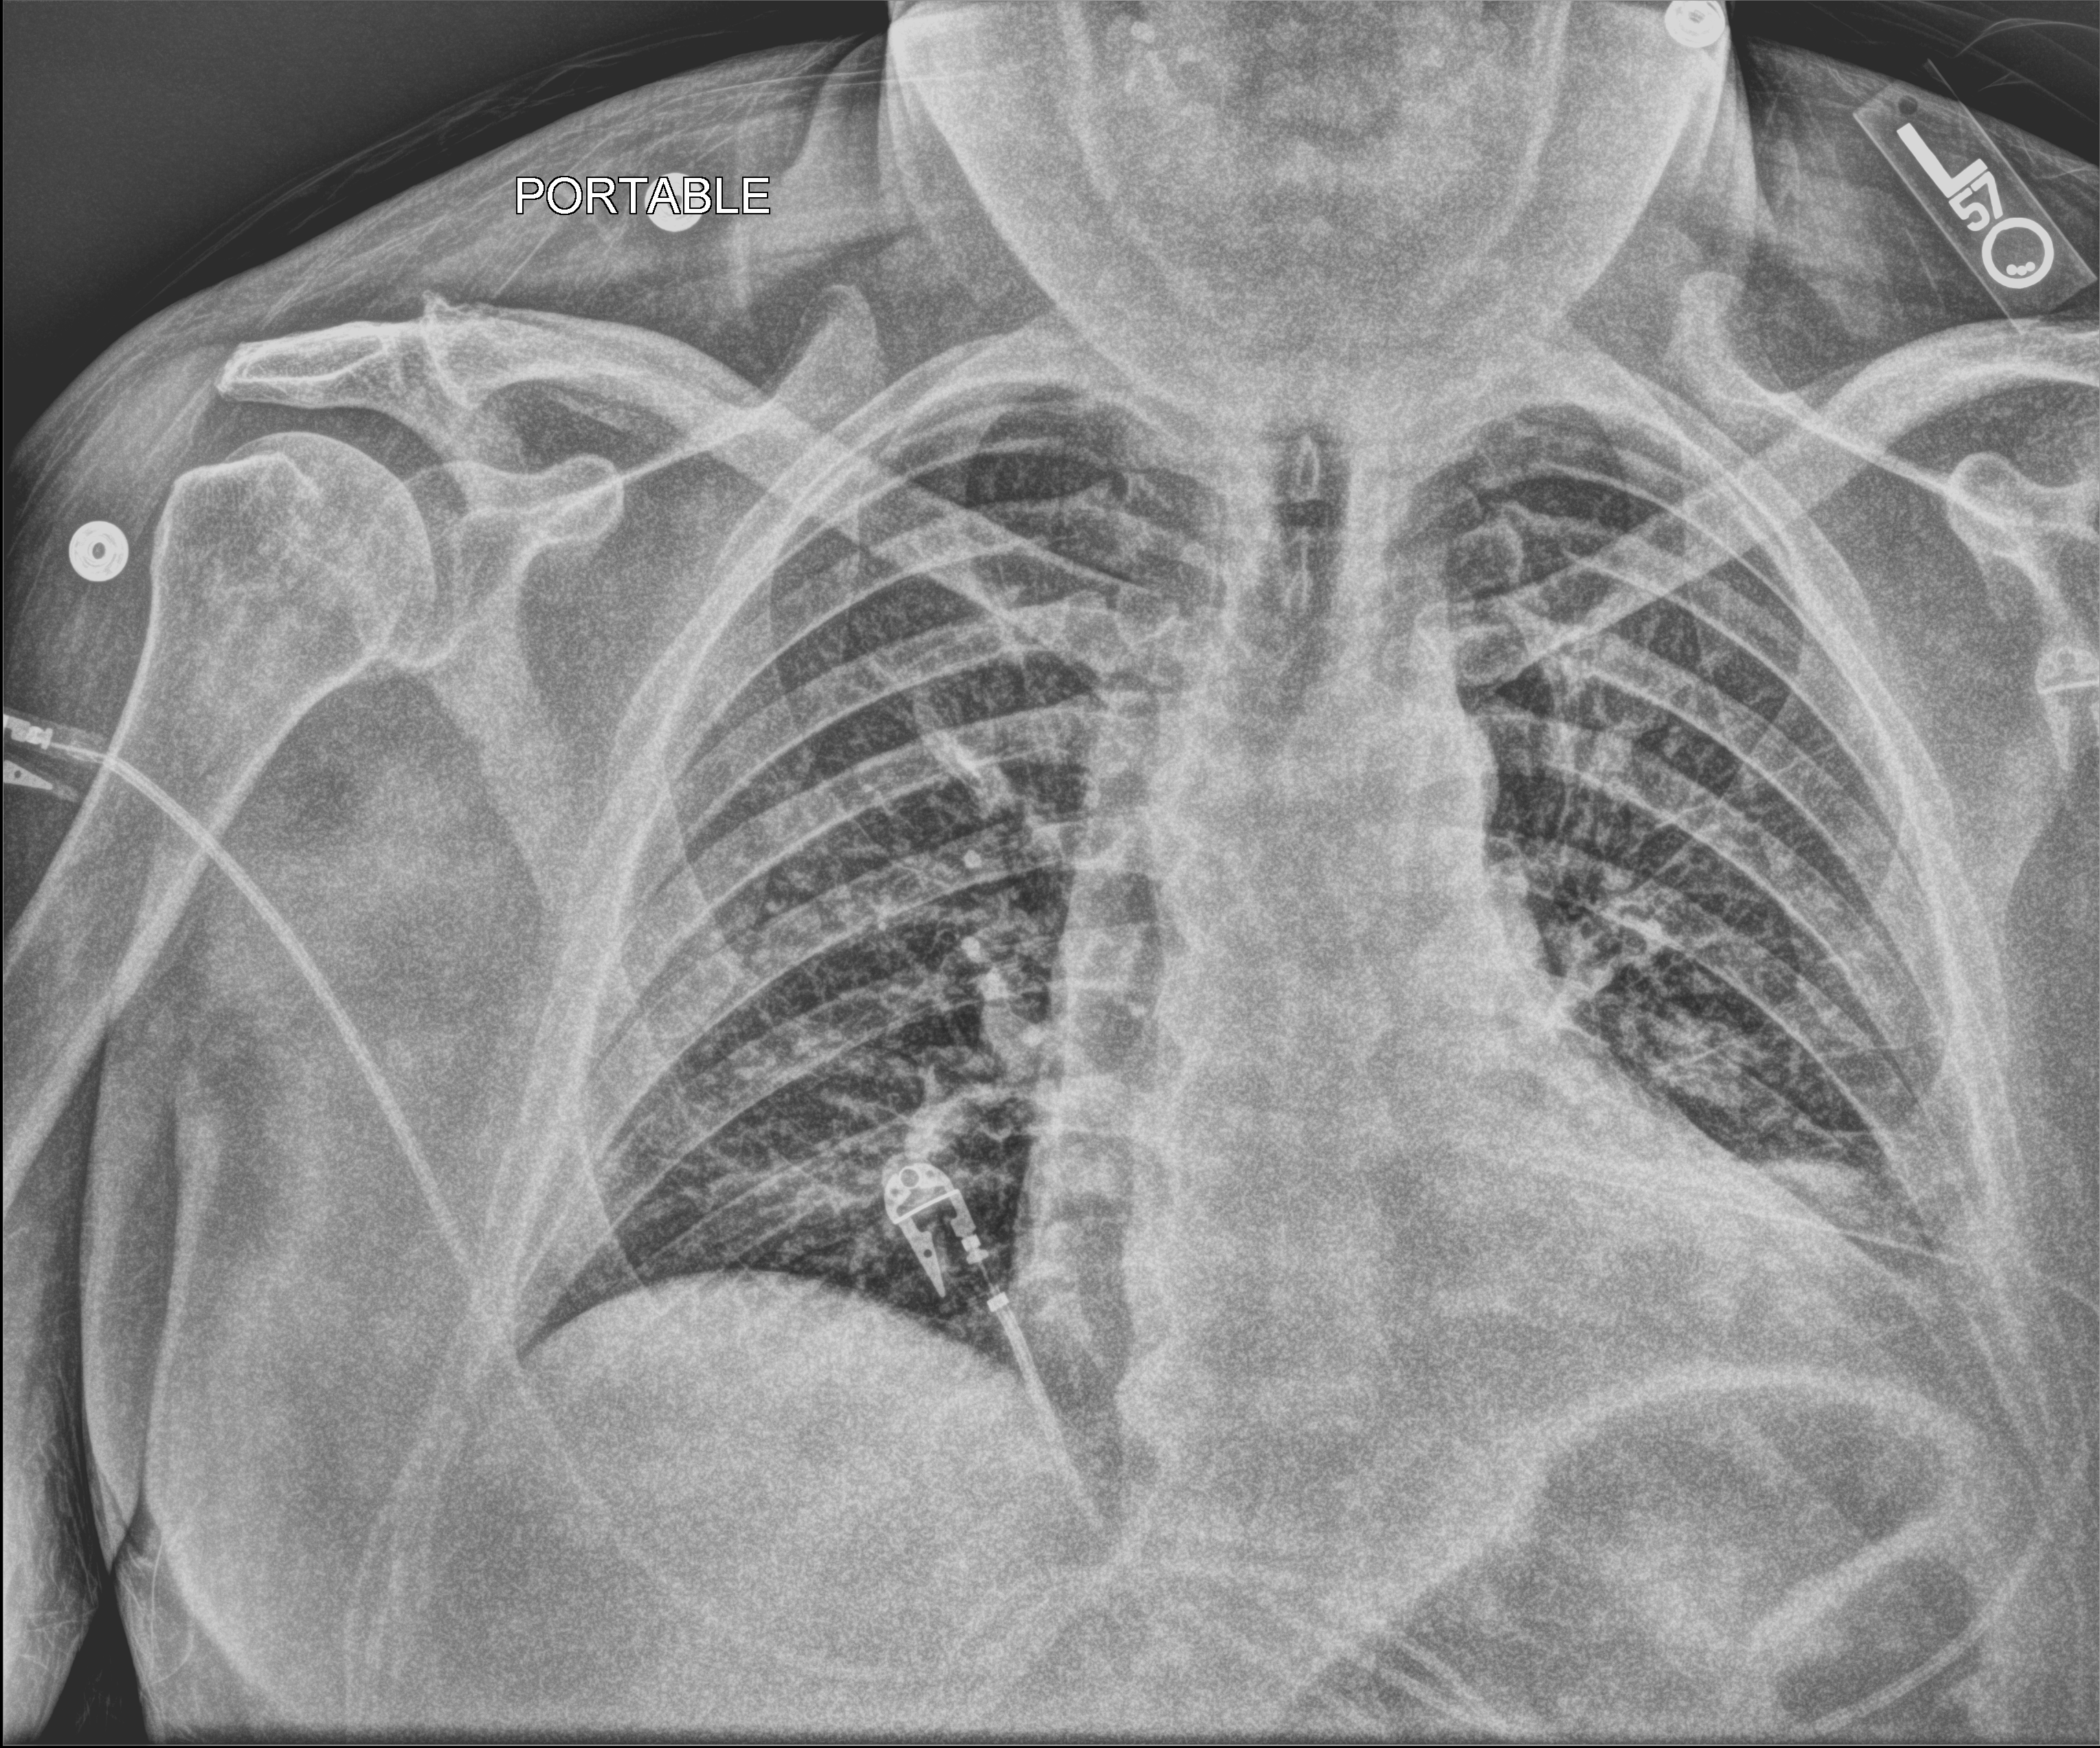
Chest X-ray (portable), anteroposterior (AP) projection. Patient hospitalised with COVID-19; male, aged 18–59 years.
Admission-level facts for this patient (not findings on this image; timing relative to this image not recorded): mechanically ventilated during this hospital stay: no; admitted to intensive care during this hospital stay: no.